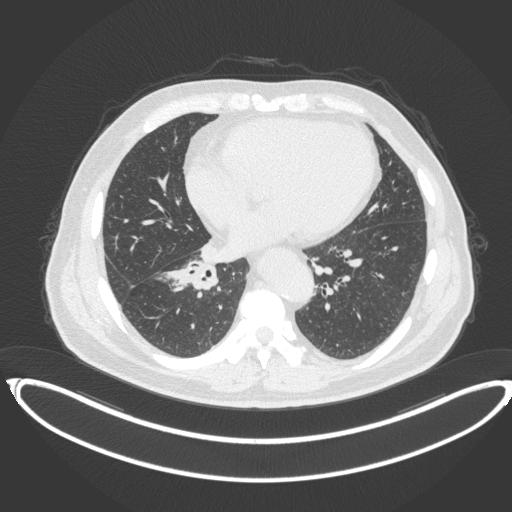
Chest CT, one axial slice. Position 165 of 383 along the scan axis. Reconstruction kernel B31f. Lung window (W 1500 / L -600 HU). 512 × 512 image matrix. Patient: male, 61 years. From the clinical record (not read from this slice): clinical TNM (as recorded): T1b N1 M0.
Structures marked on this image (rectangle marked by the reading radiologist):
- lung tumour (recorded histology: squamous cell carcinoma): bounding box [x1, y1, x2, y2] px = [180, 259, 218, 292]